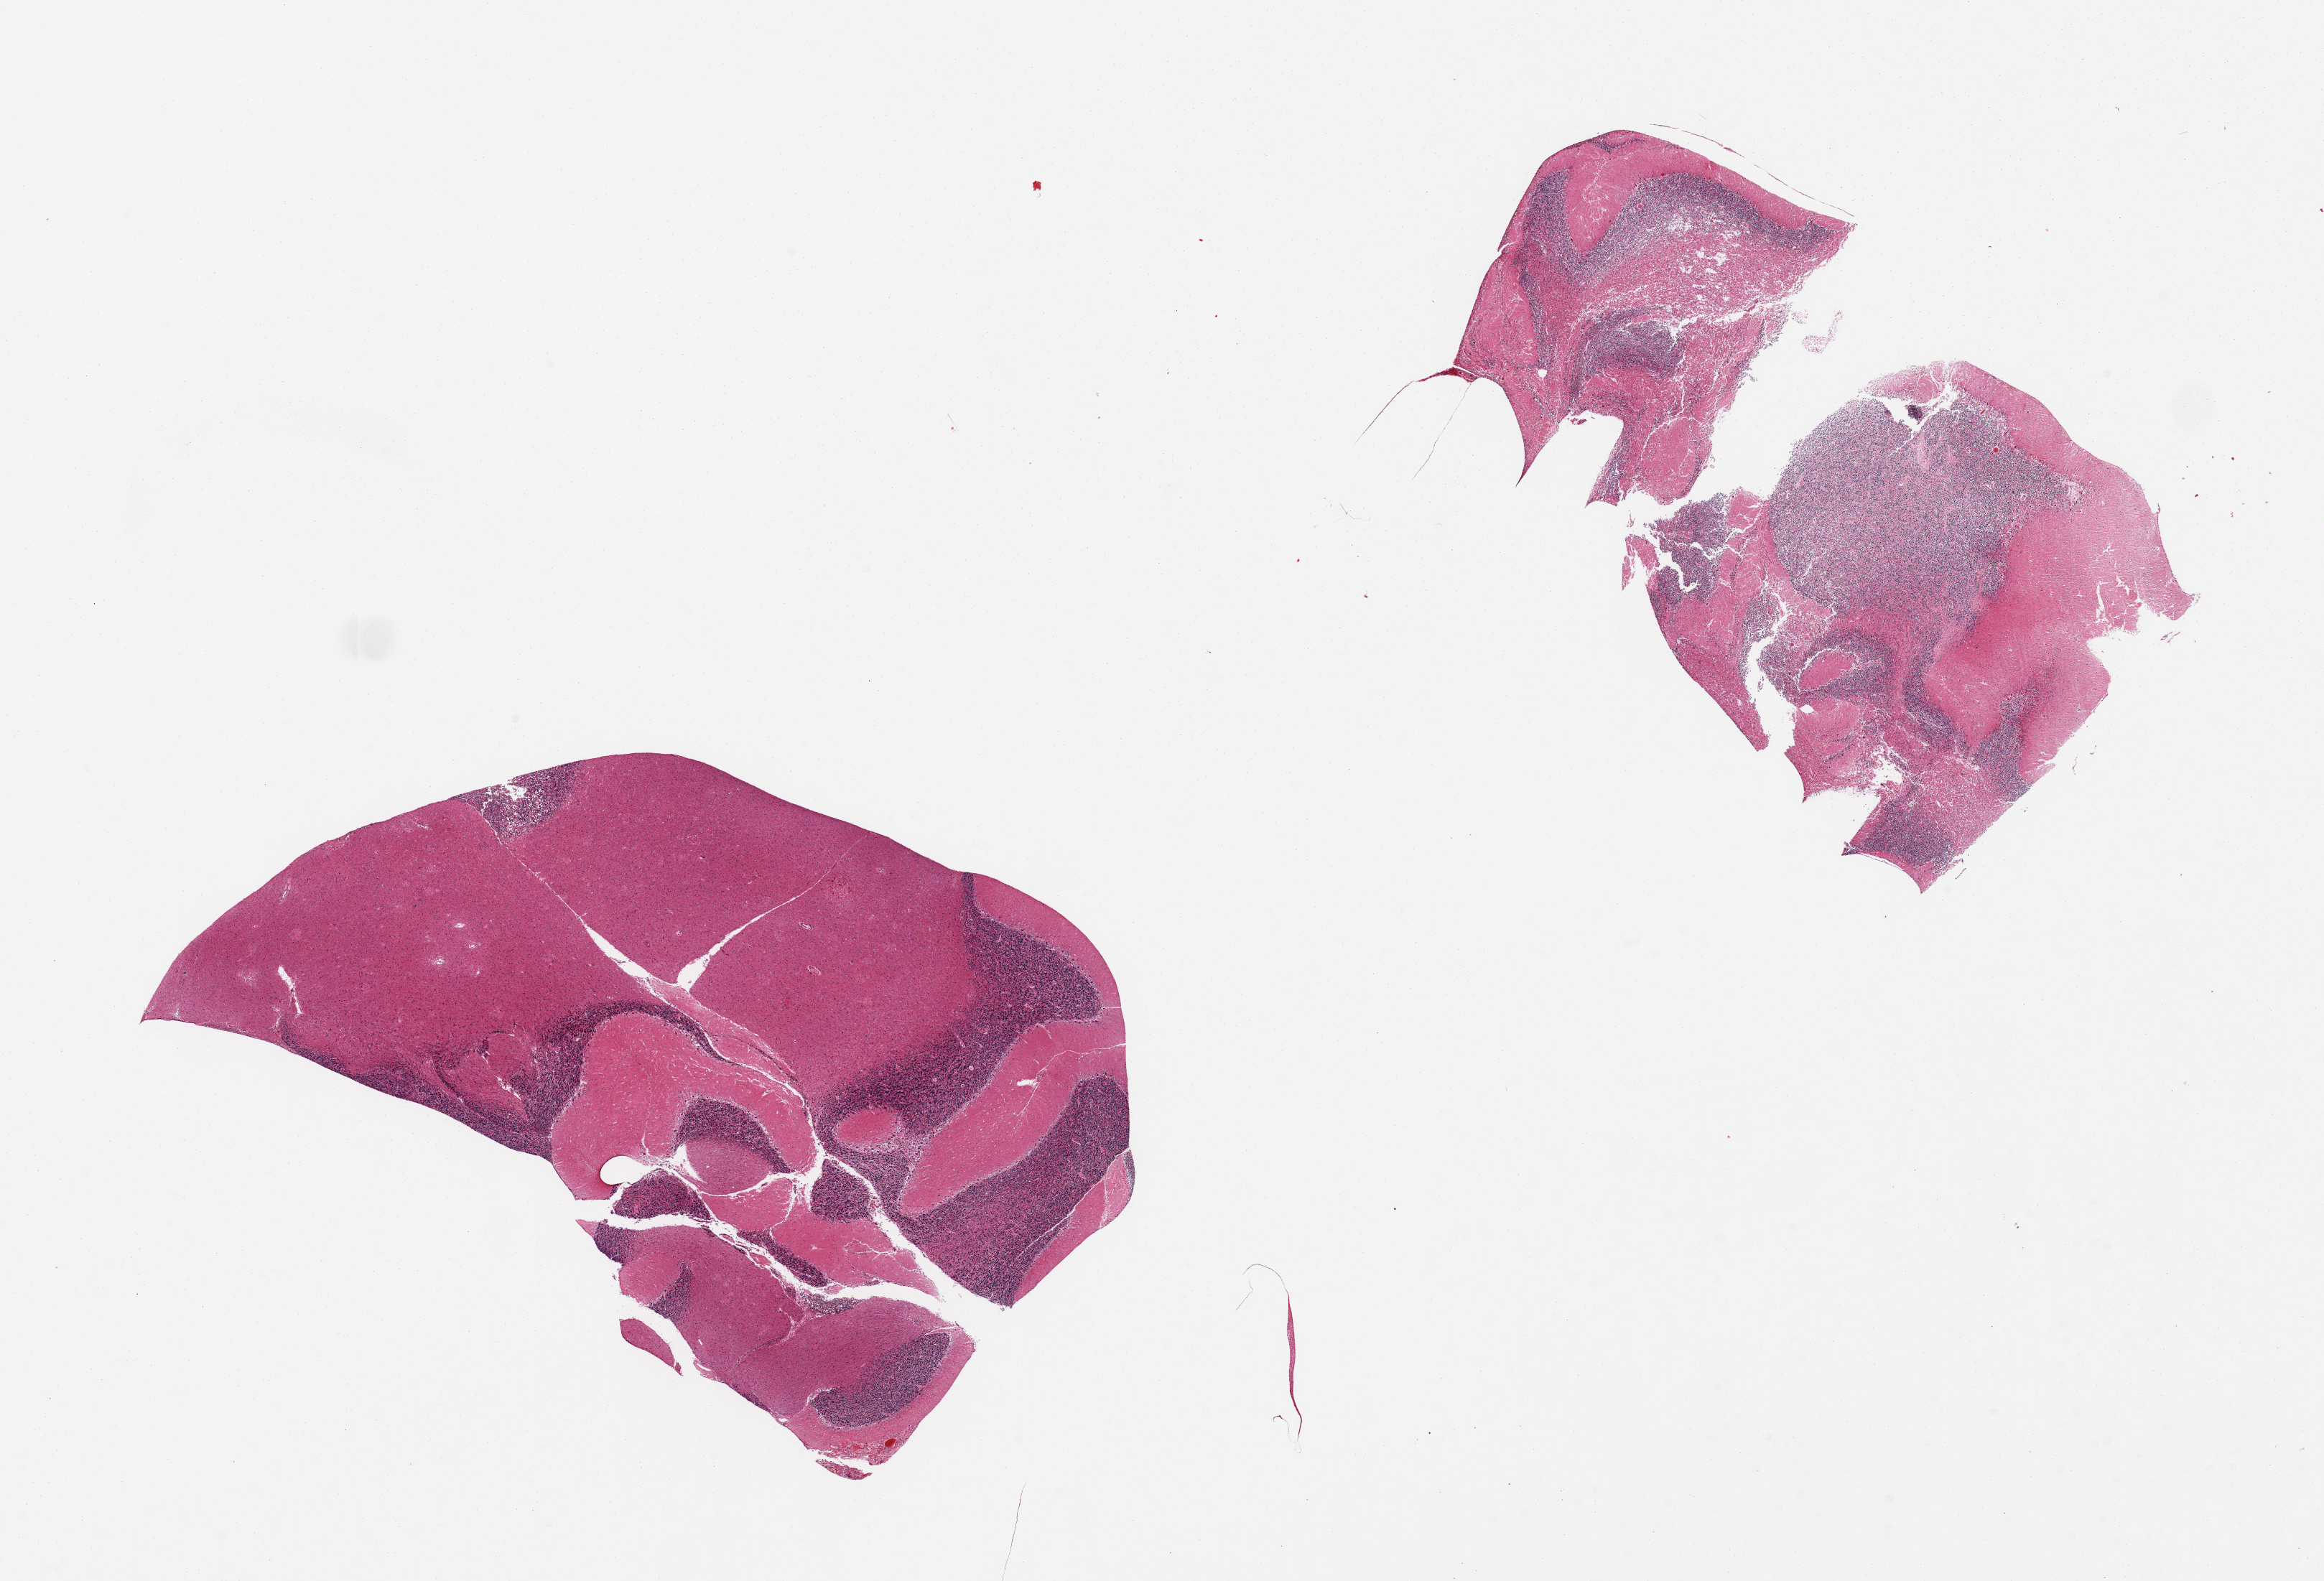
Digitized haematoxylin and eosin-stained section, brightfield, a low-resolution overview of the entire scanned area, about 25.6 x 17.4 mm (from a 20x scan). PAXgene-fixed, paraffin-embedded tissue. Sampled site (target tissue): cerebellum. Donor tissue sample. Male donor.
* review note (as recorded): 2 pieces, no abnormalities; Purkinje cells look good